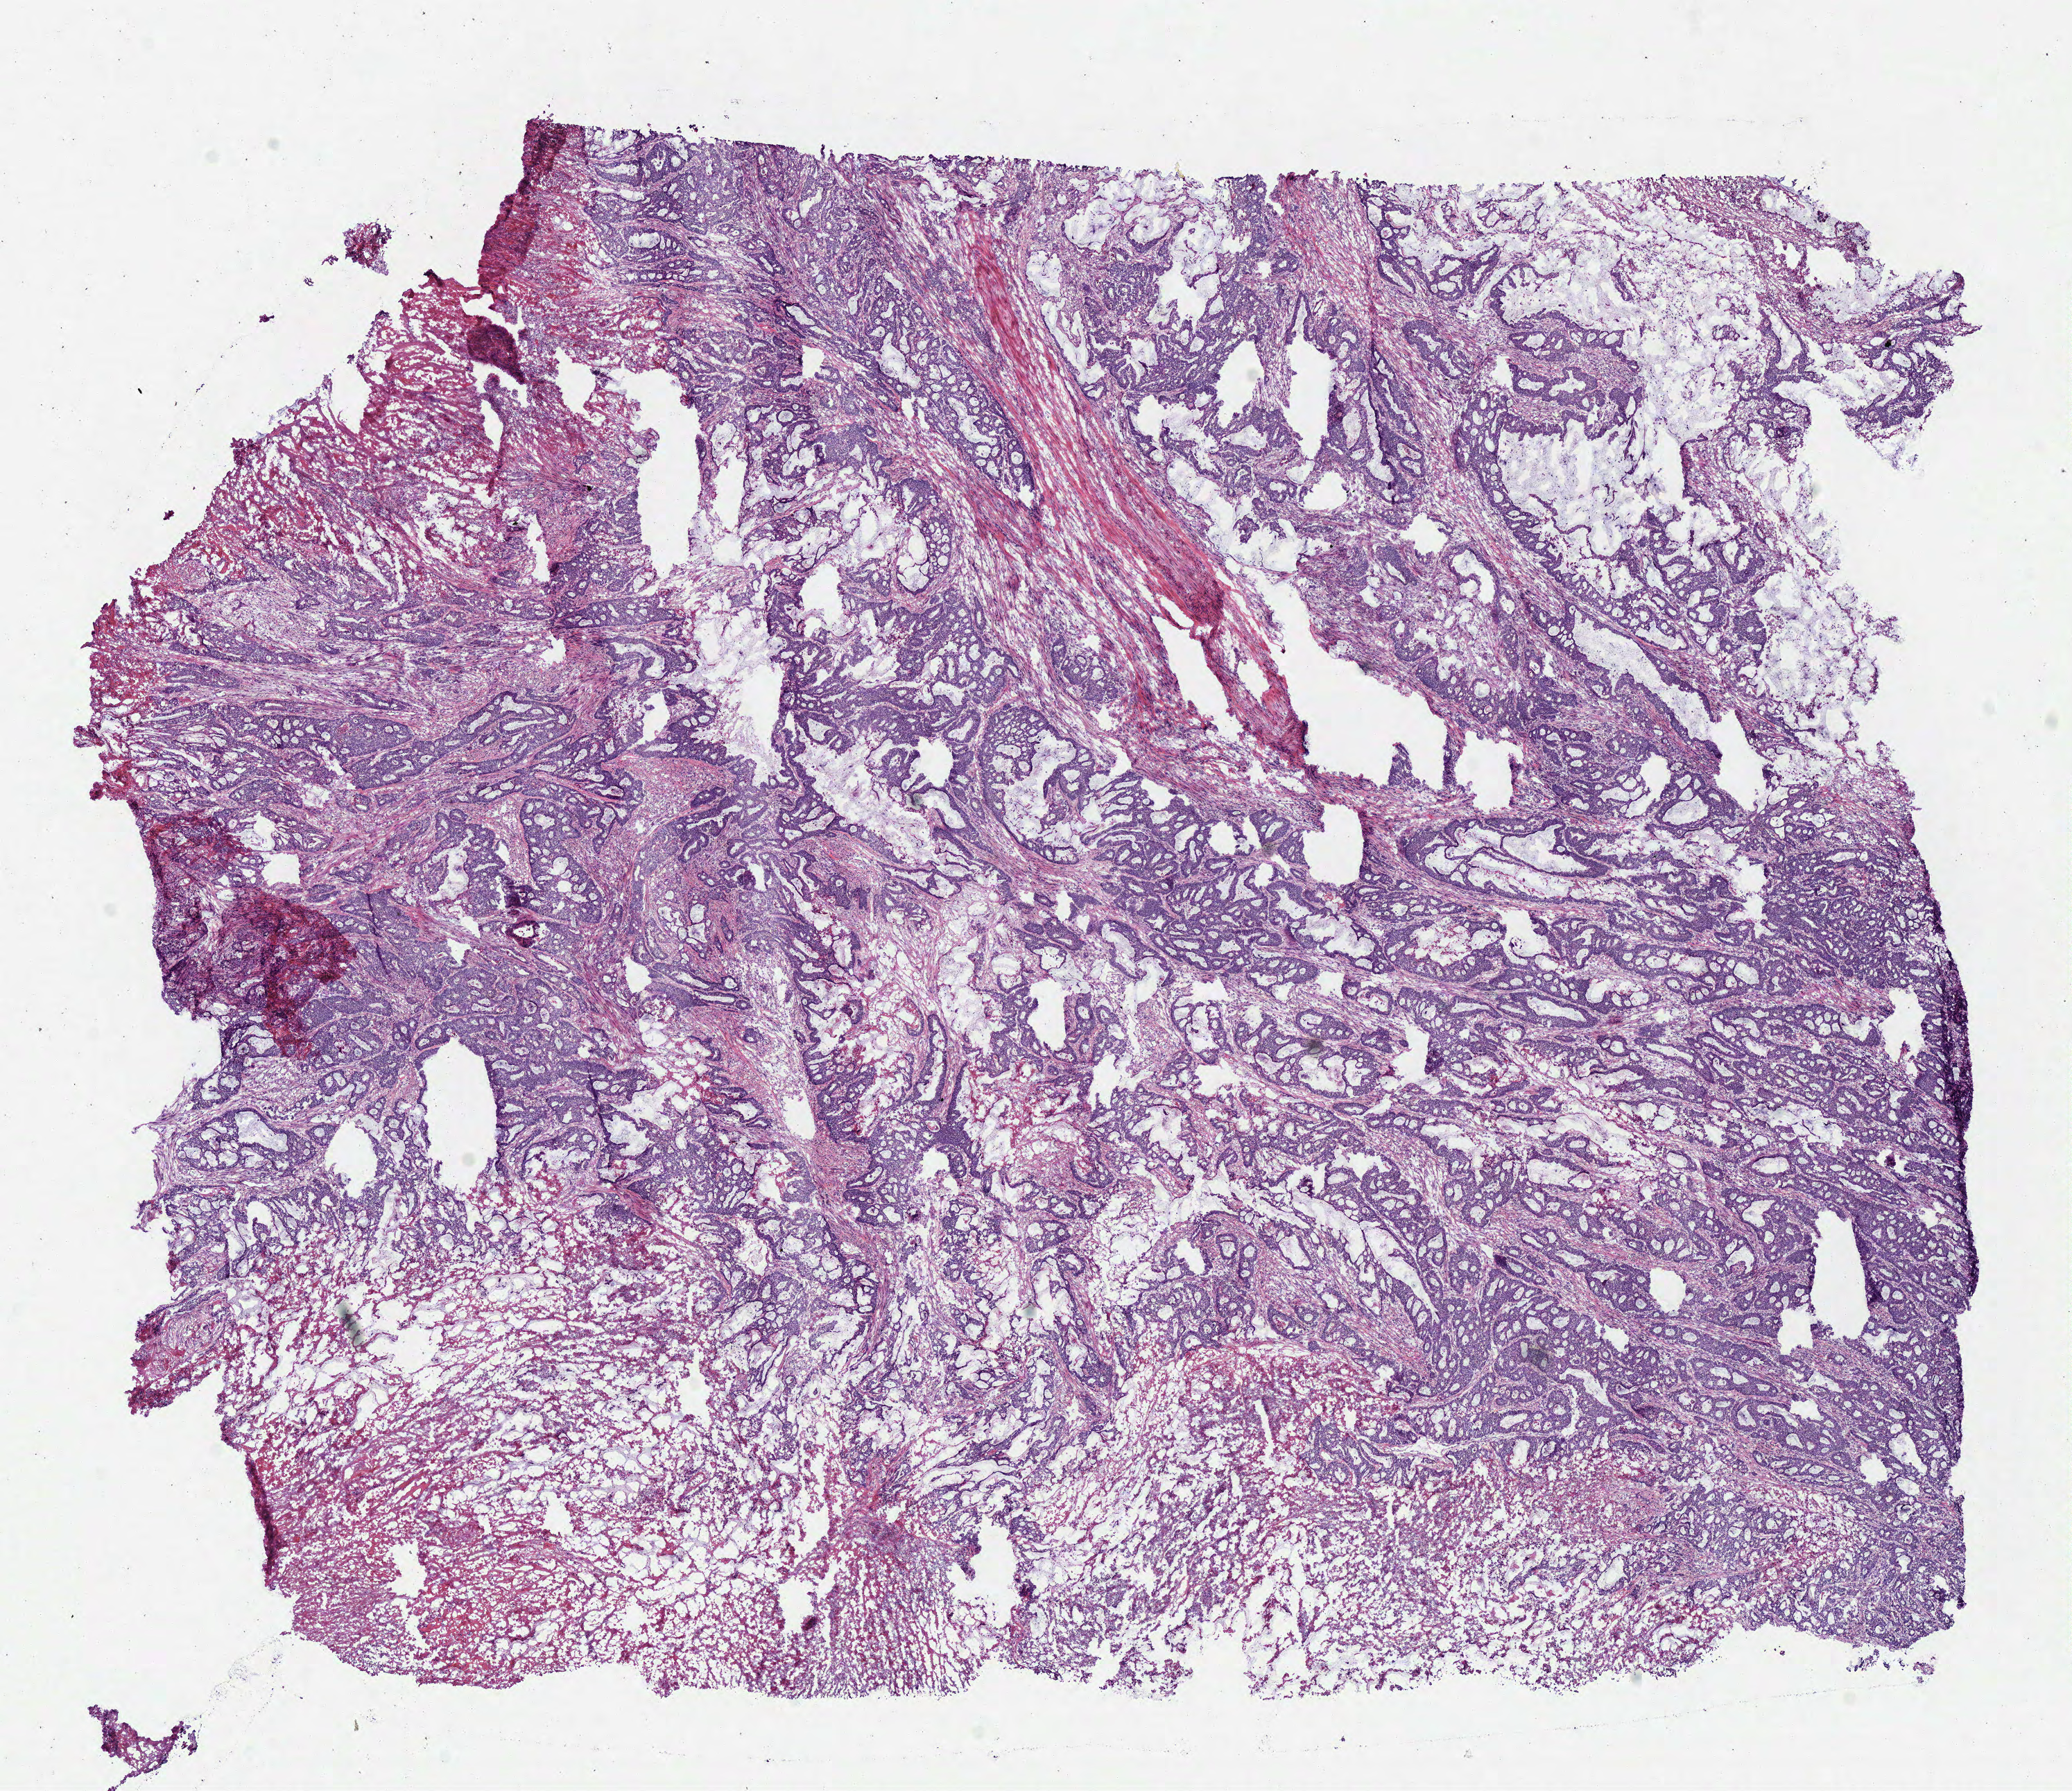
Digitized H&E tissue section (whole slide), shown as a low-resolution overview of the whole scanned area (about 11.7 x 10.2 mm). Frozen section from the bottom of the tissue portion. Primary tumour sample from the rectum. Male, age 60 years at initial diagnosis. Composition of this section per pathologist review: tumour cells 65%, tumour nuclei 80%, normal cells 0%, stromal cells 15%, necrosis 20%.
AJCC pathologic stage: IIA (7th edition). Pathologic diagnosis: Mucinous adenocarcinoma. TNM: T3 N0 M0. Lymph nodes positive (case pathology): 0 of 25 examined.